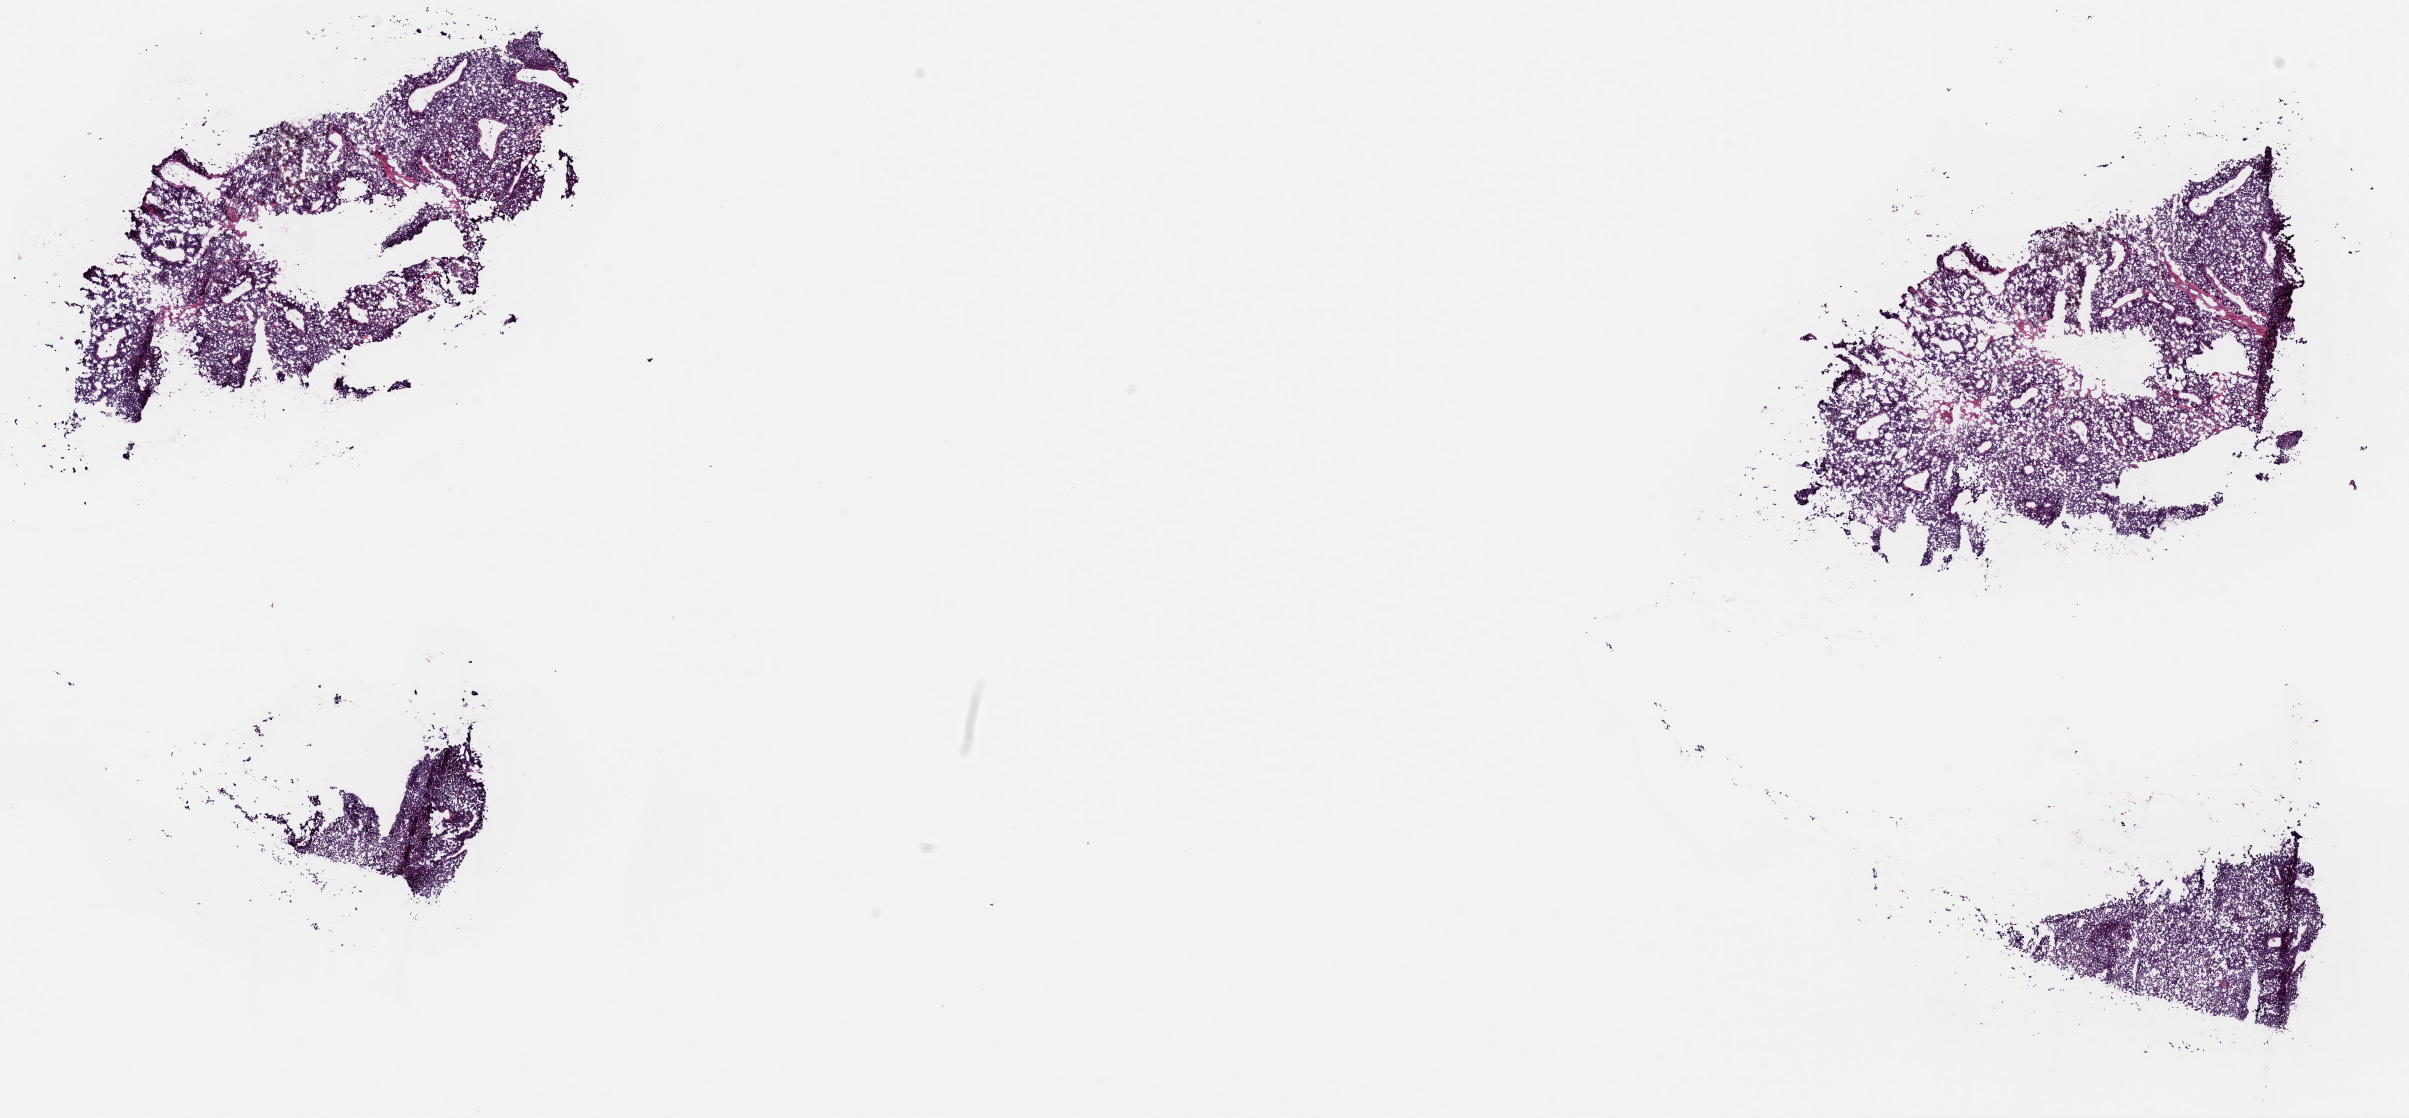
H&E whole-slide image, shown as a low-resolution overview of the whole scanned area (about 19.0 x 8.8 mm, from a 40x scan); frozen section from the top of the tissue portion; metastatic tumour sample, sampled site not recorded. Patient: female, age at initial diagnosis 47 years. Pathologist review of this section (percent, as recorded): tumour cells 90%, tumour nuclei 90%, normal cells 0%, stromal cells 6%, necrosis 4%. Inflammatory infiltration, as recorded: lymphocyte infiltration 1%, monocyte infiltration 1%, neutrophil infiltration 0%.
- this section: metastatic tumour tissue
- patient diagnosis: Malignant melanoma, NOS